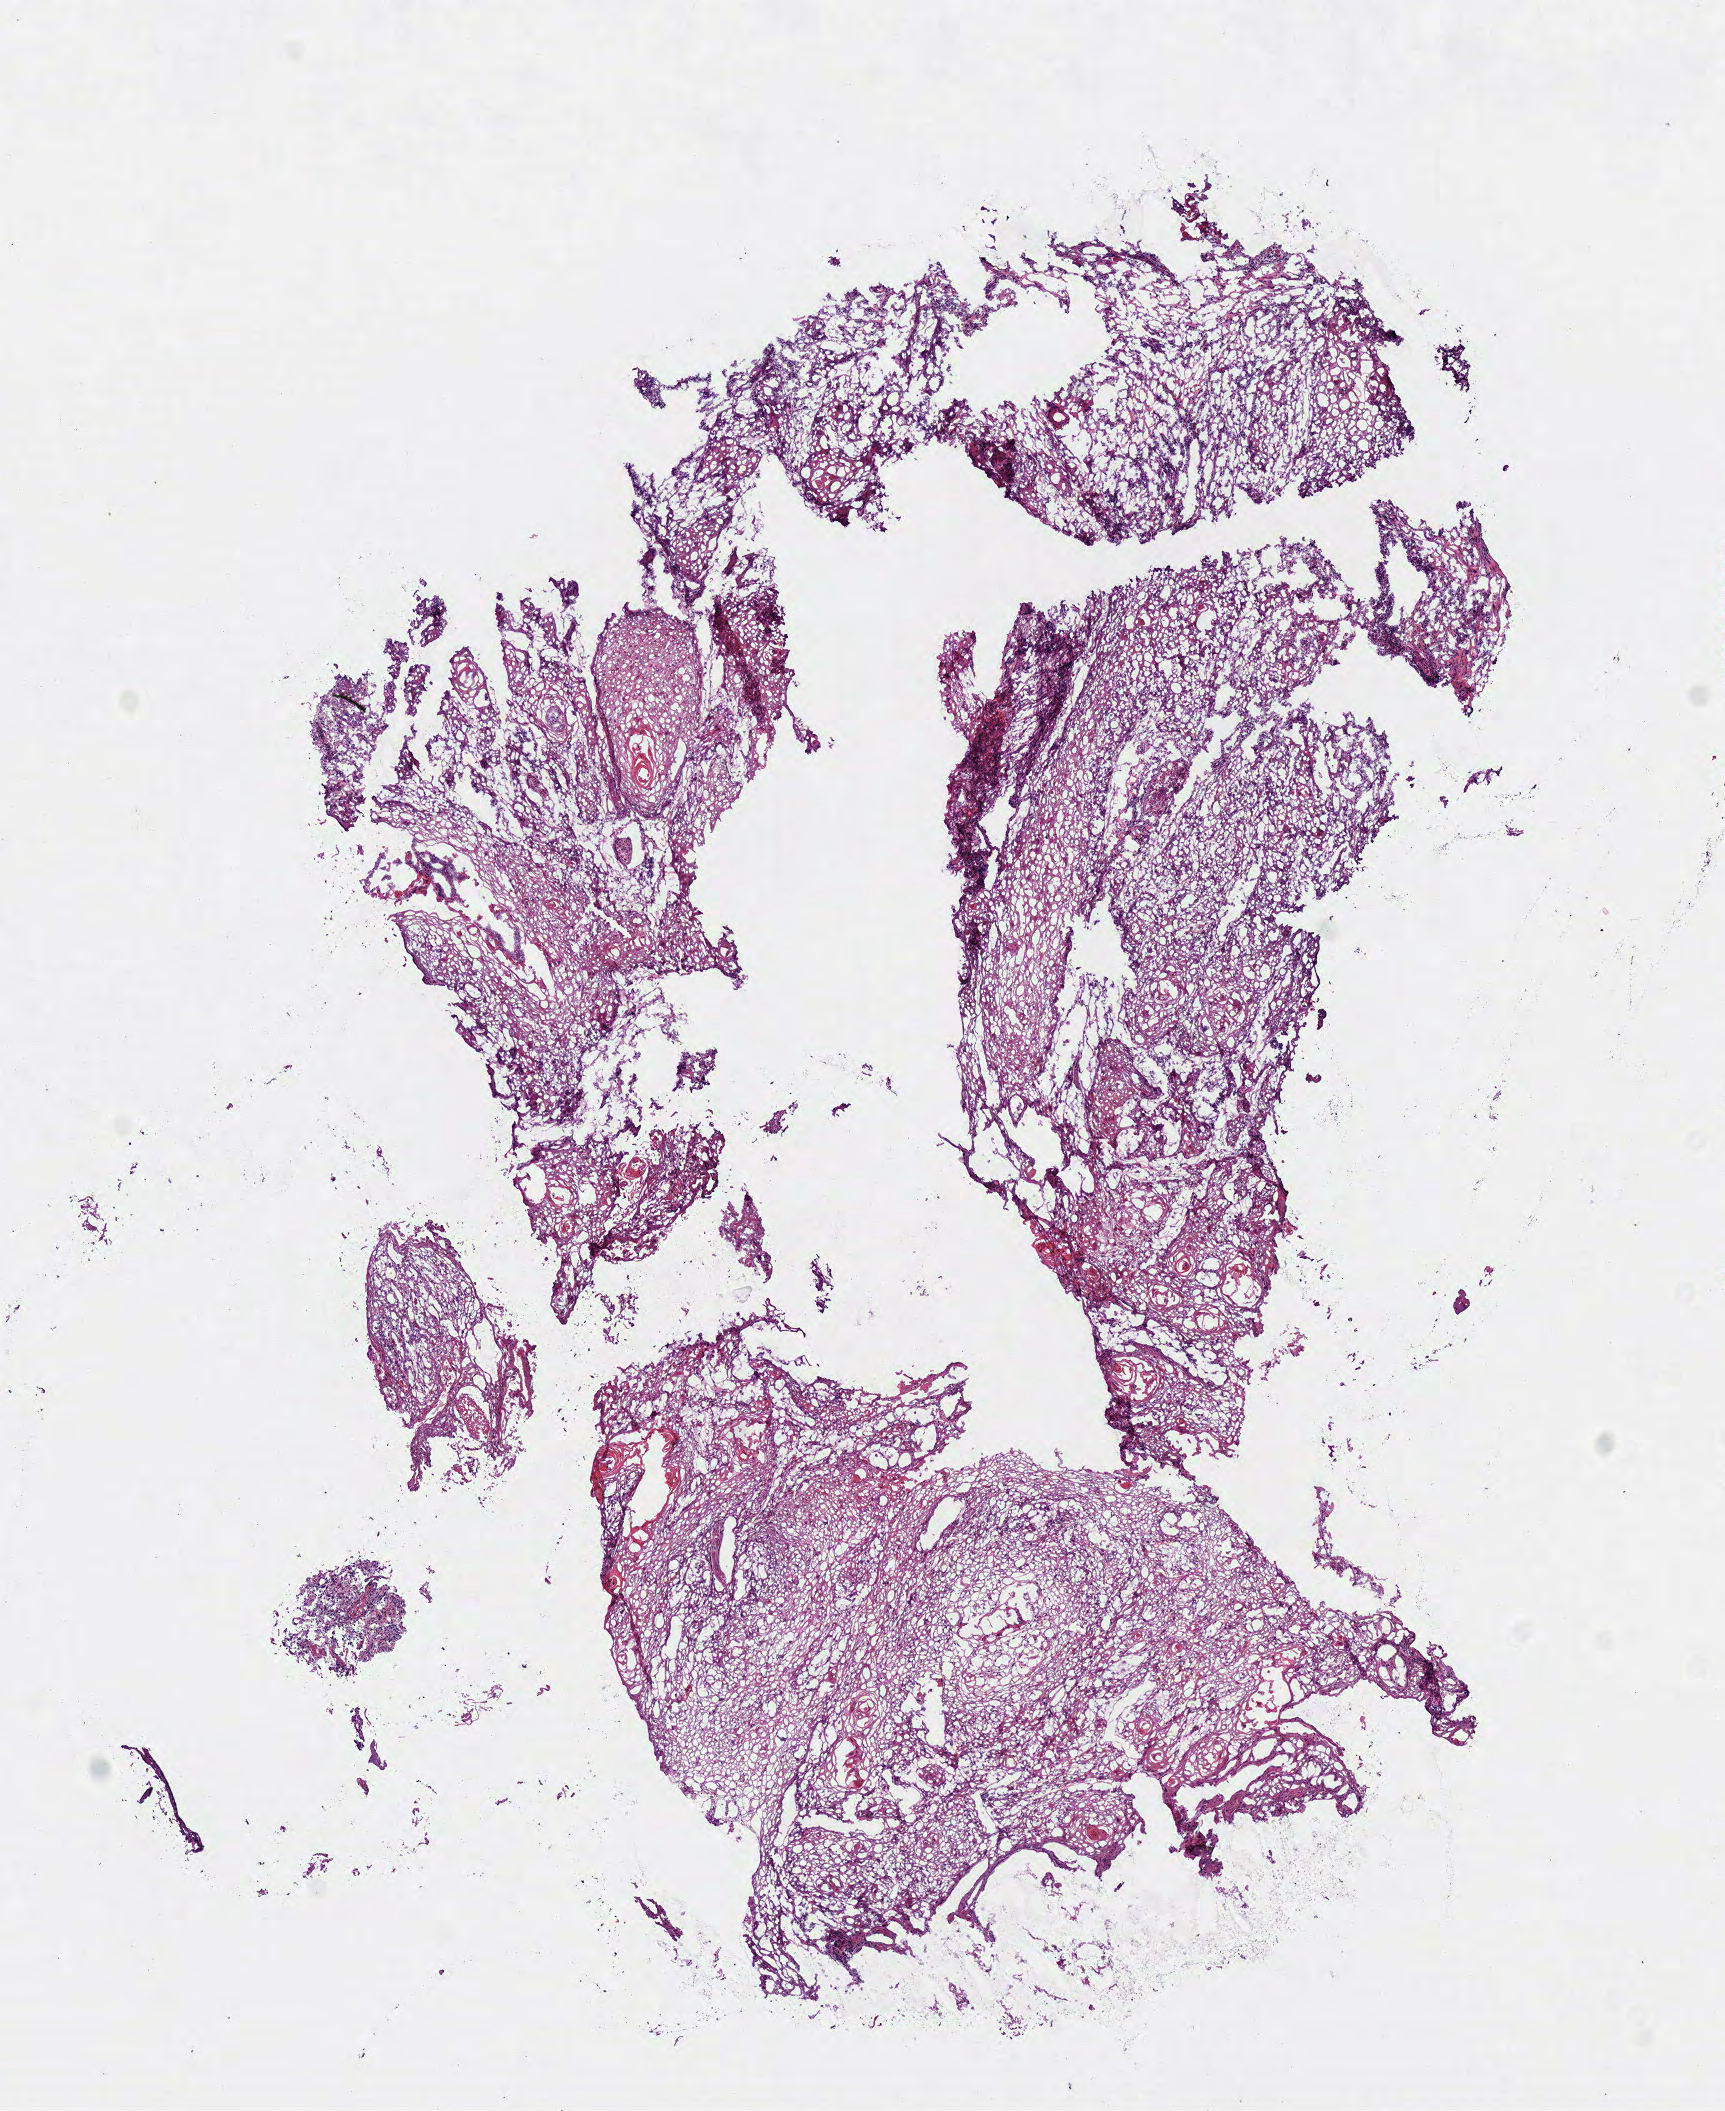
Whole-slide histology image, H&E — whole scanned area (about 6.8 x 8.3 mm, from a 40x scan) shown as a low-resolution overview; frozen section from the top of the tissue portion; sample: primary tumour, head and neck. Patient: female, age at initial diagnosis 62 years. Histologic grade: G3 (poorly differentiated). Pathologist review of this section (percent, as recorded): tumour cells 95%, tumour nuclei 85%, normal cells 0%, stromal cells 5%, necrosis 0%.
AJCC pathologic stage: III (7th edition). Diagnosis: Squamous cell carcinoma, NOS. Lymph nodes positive (case pathology): 1 of 58 examined.